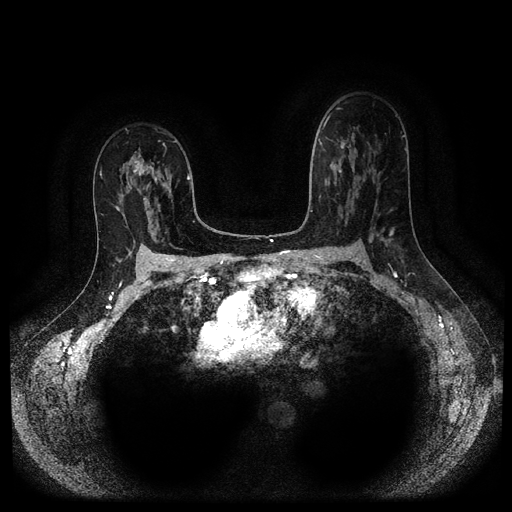
Breast MRI (dynamic contrast-enhanced, multi-phase), one axial slice. Slice 63 of 116 in the series (ordered by position). Dynamic contrast-enhanced series, time point 2 of 5 at this slice position (early post-contrast). 1.5 T. TE 2.6 ms, TR 5.3 ms. 2.2 mm slice thickness. 512 × 512 image matrix, field of view 340 × 340 mm. Patient: female, 50 years.
Outlined on this slice (semi-automatically segmented with operator editing):
- breast lesion (labelled 'tumour' in the annotation; benign lesions carry a separate 'benign' label): box from (x=132, y=148) to (x=161, y=180) px